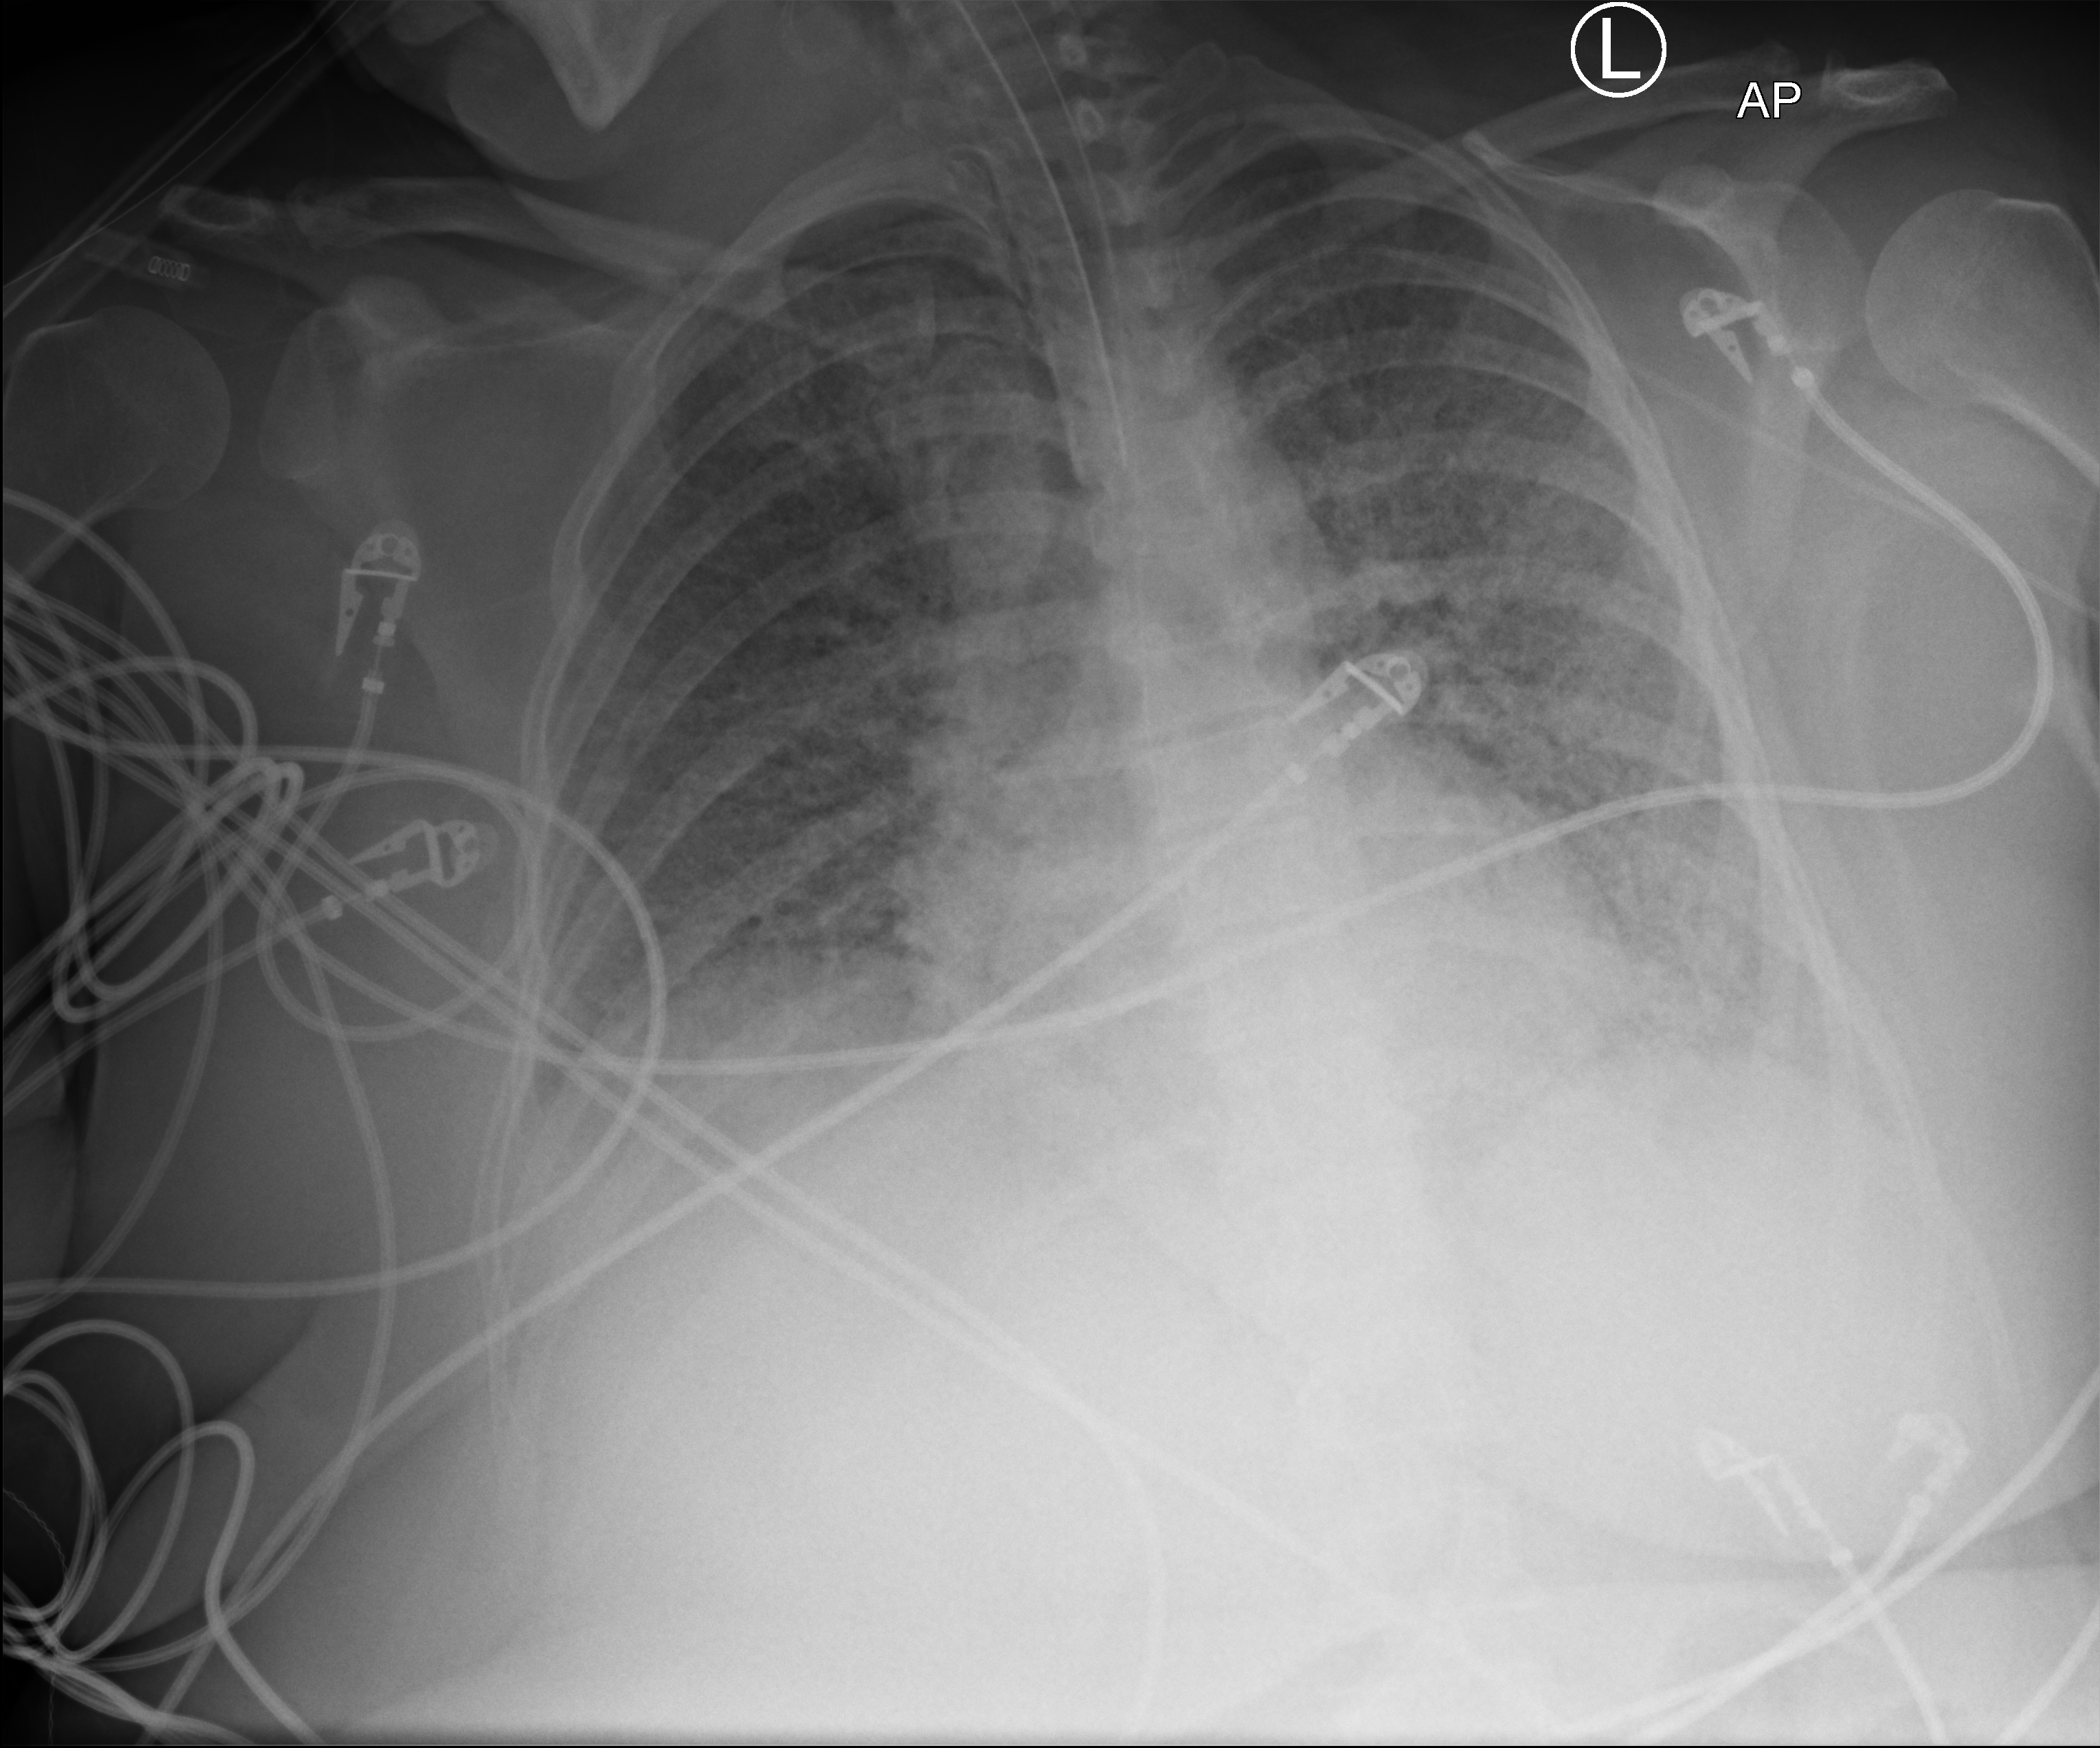
Bedside chest radiograph (computed radiography), anteroposterior (AP) projection. Patient hospitalised with COVID-19; female, aged 18–59 years.
Hospital-stay facts (about this admission, not read from this image; timing relative to this image not recorded):
- mechanically ventilated during this hospital stay: yes